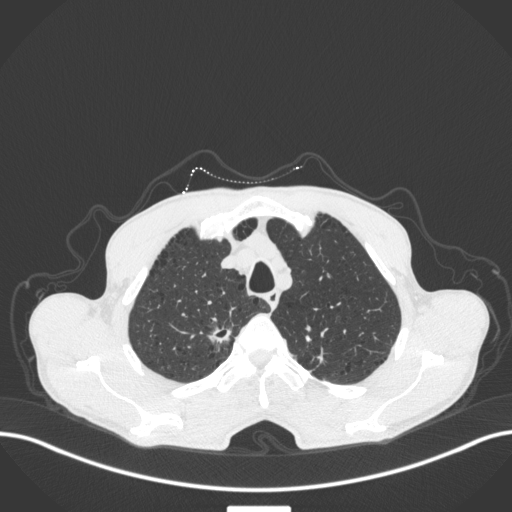
Chest CT, one axial slice; position 357 of 445 along the scan axis; lung window (W 1500 / L -600 HU); 1 mm slice thickness; 512 × 512 image matrix. Male patient, age 70 years. Case-level facts recorded for this patient, not image findings: clinical TNM (as recorded): T1a N0 M0.
Outlined on this slice (rectangle marked by the reading radiologist):
- lung tumour (recorded histology: adenocarcinoma): box from (x=203, y=321) to (x=237, y=353) px